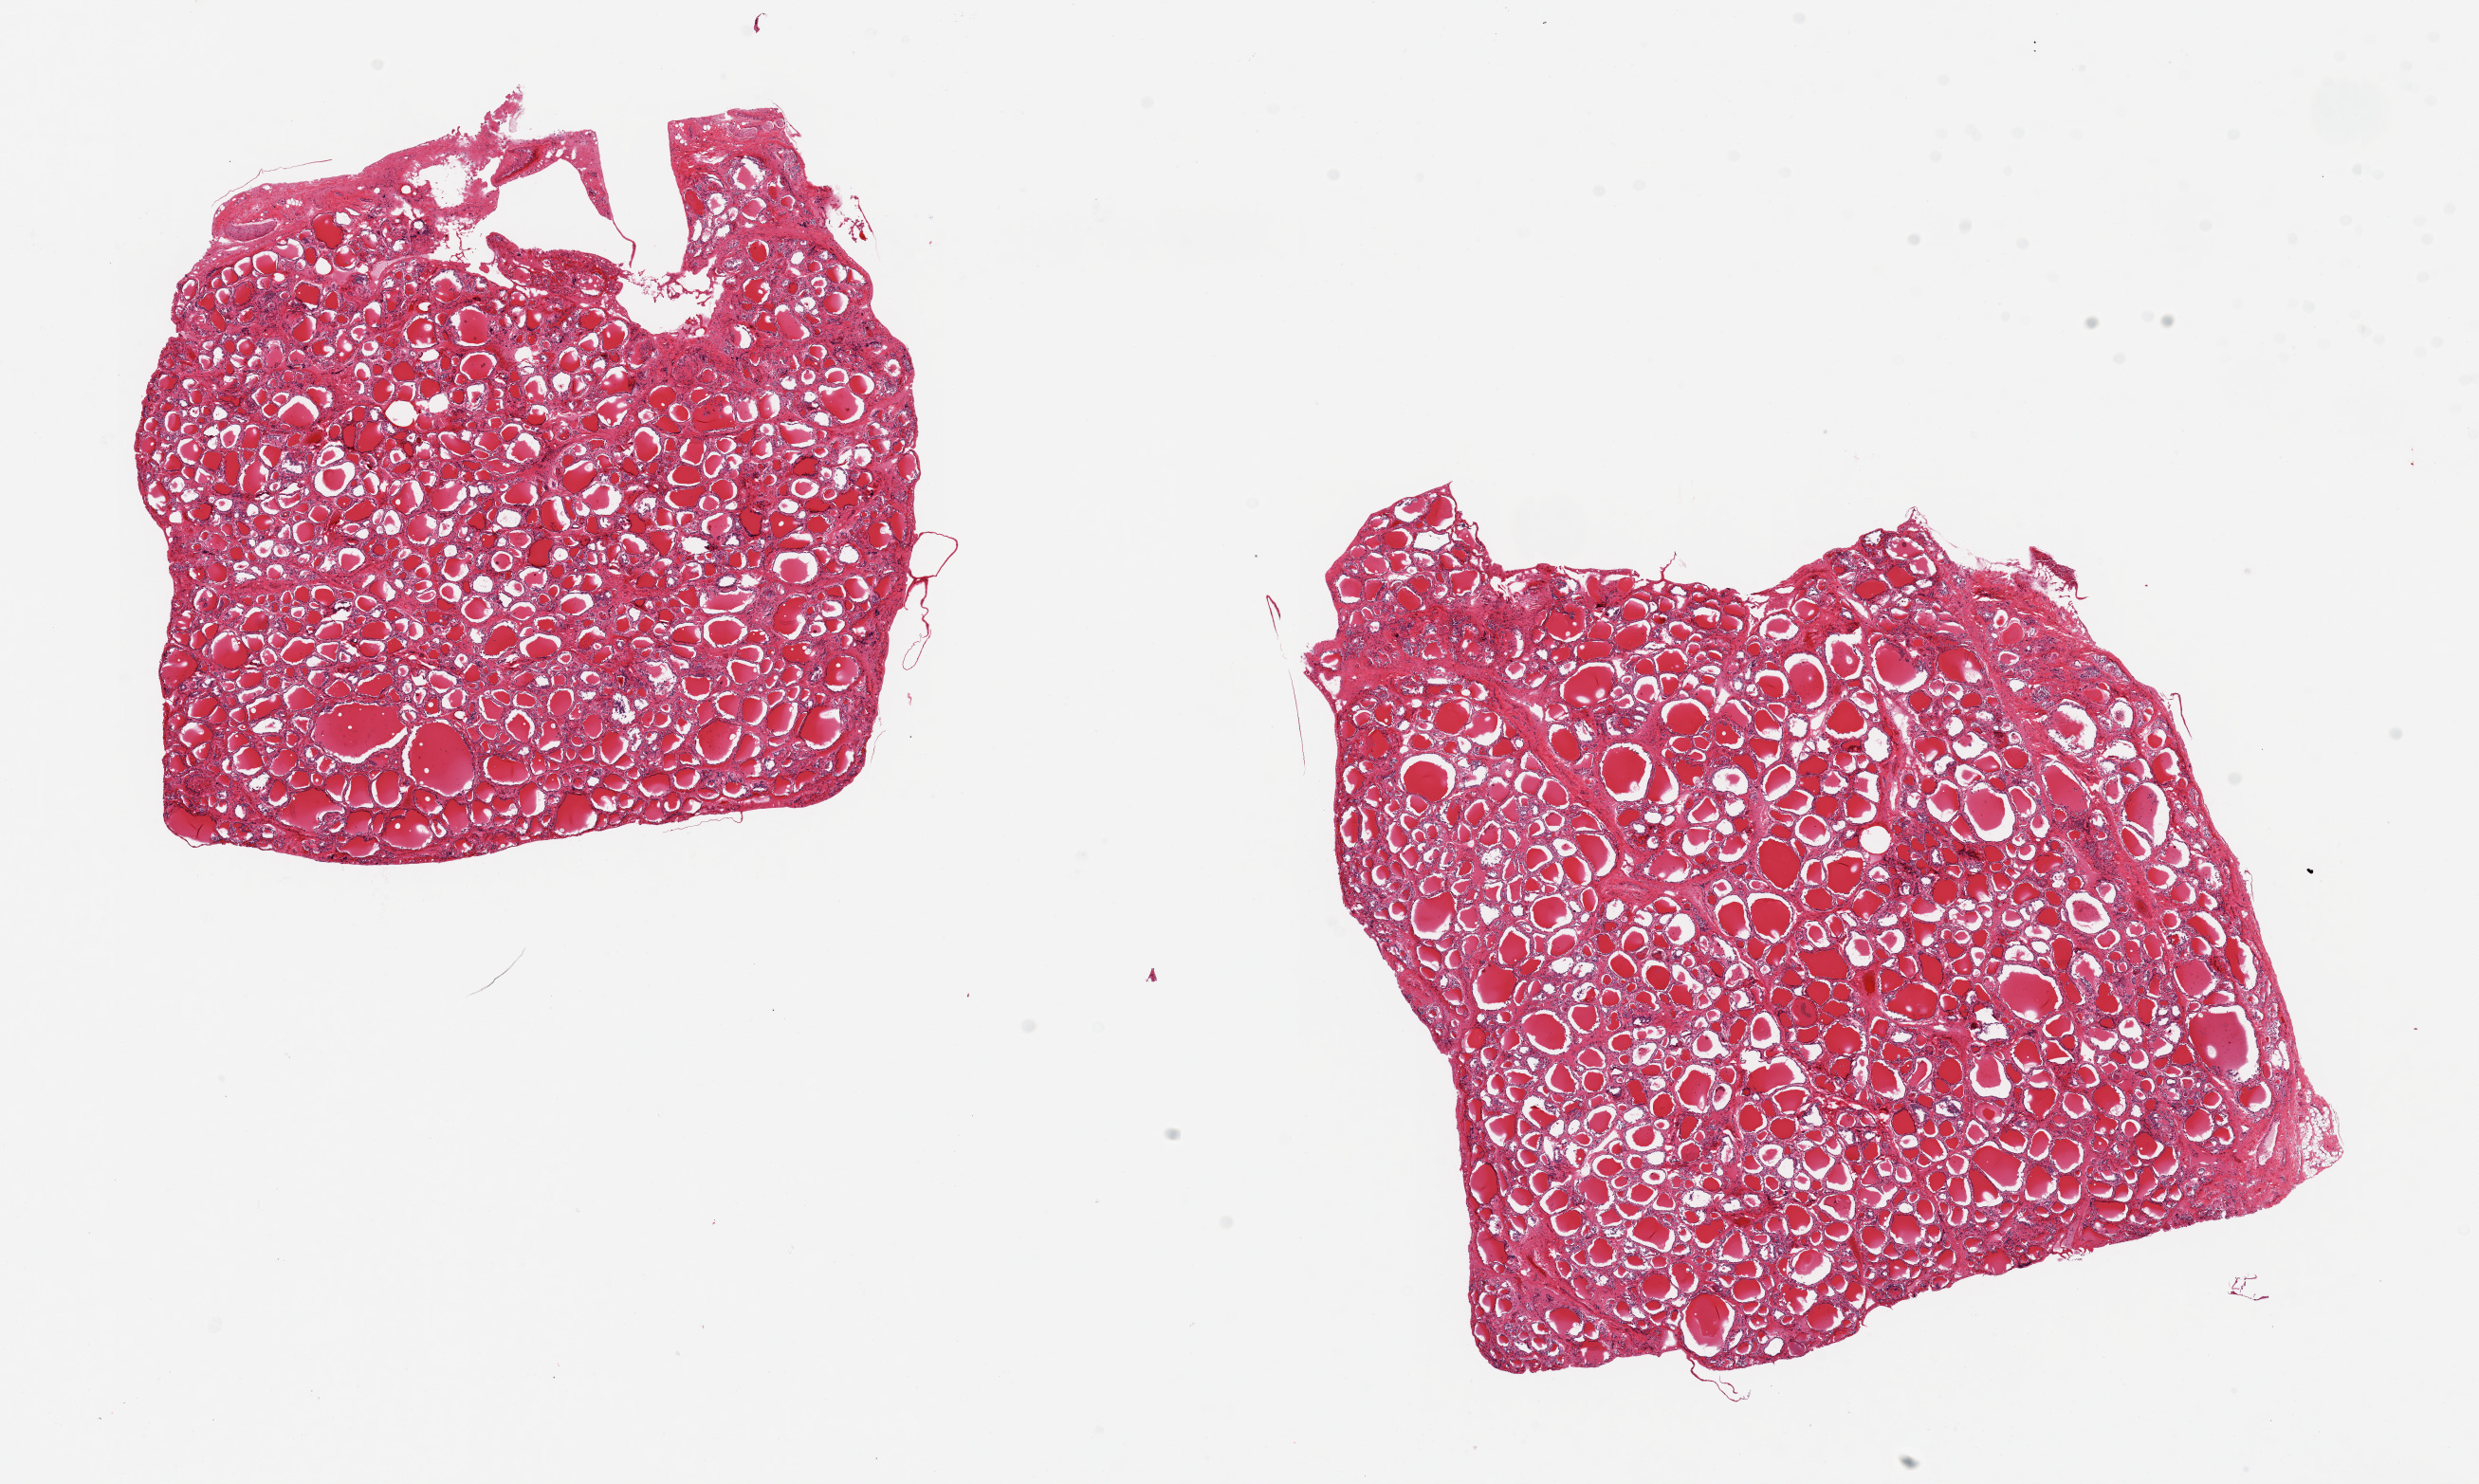
H&E whole-slide image — low-resolution overview of the scanned area, about 20.7 x 12.4 mm (slide scanned at 20x). PAXgene-fixed paraffin-embedded (PFPE) section. Sampled site (target tissue): thyroid. Tissue donor sample. Donor: male.
Reviewer comment on this tissue sample: 2 pieces ~6x6mm.